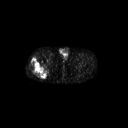
FDG PET of an extremity soft-tissue mass (from a PET/CT study), one axial slice; slice 265 of 267 in the series (ordered by position); 128 × 128 image matrix, field of view 700 × 700 mm. Patient: male, 43 years. Case-level facts recorded for this patient, not image findings: histological type: poorly differentiated synovial sarcoma; grade: high; site of the primary tumour: right buttock.
Annotated regions visible in this slice (expert contour drawn on MRI and transferred to this co-registered scan by the dataset authors):
- gross tumour volume including surrounding oedema: bounding box <29,58,50,78> (left, top, right, bottom; pixels)
- gross tumour volume (mass): <29,58,48,78>